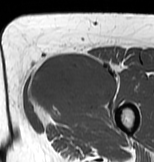
MRI of an extremity soft-tissue mass, one axial slice. Position 31 of 83 along the scan axis. MR volume resampled by the dataset authors to the PET/CT grid (not the native acquisition matrix). 3.27 mm slice thickness. 154 × 162 image matrix, field of view 150 × 158 mm. Female patient. From the clinical record (not read from this slice): histological type: myxofibrosarcoma; grade: intermediate; site of the primary tumour: left thigh.
Structures marked on this image (expert contour drawn on MRI and transferred to this co-registered scan by the dataset authors):
- gross tumour volume including surrounding oedema: box from (x=26, y=52) to (x=120, y=128) px
- gross tumour volume (mass): (x=28, y=52)–(x=116, y=113)